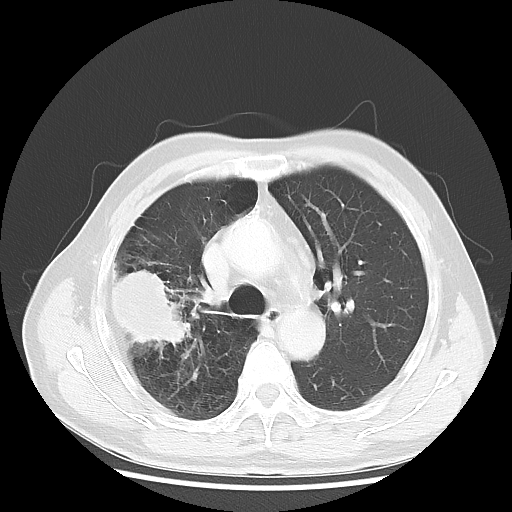
Chest CT, one axial slice; slice 33 of 50 in the series (ordered by position); reconstruction kernel LUNG; lung window (W 1500 / L -600 HU); 5 mm slice thickness; 512 × 512 image matrix, field of view 360 × 360 mm. Patient: male, 69 years. From the clinical record (not read from this slice): clinical TNM (as recorded): T3 N0 M0; histopathological grade: G3.
Structures marked on this image (bounding box drawn by a radiologist):
- lung tumour (recorded histology: adenocarcinoma): bounding box <111,268,196,353> (left, top, right, bottom; pixels)